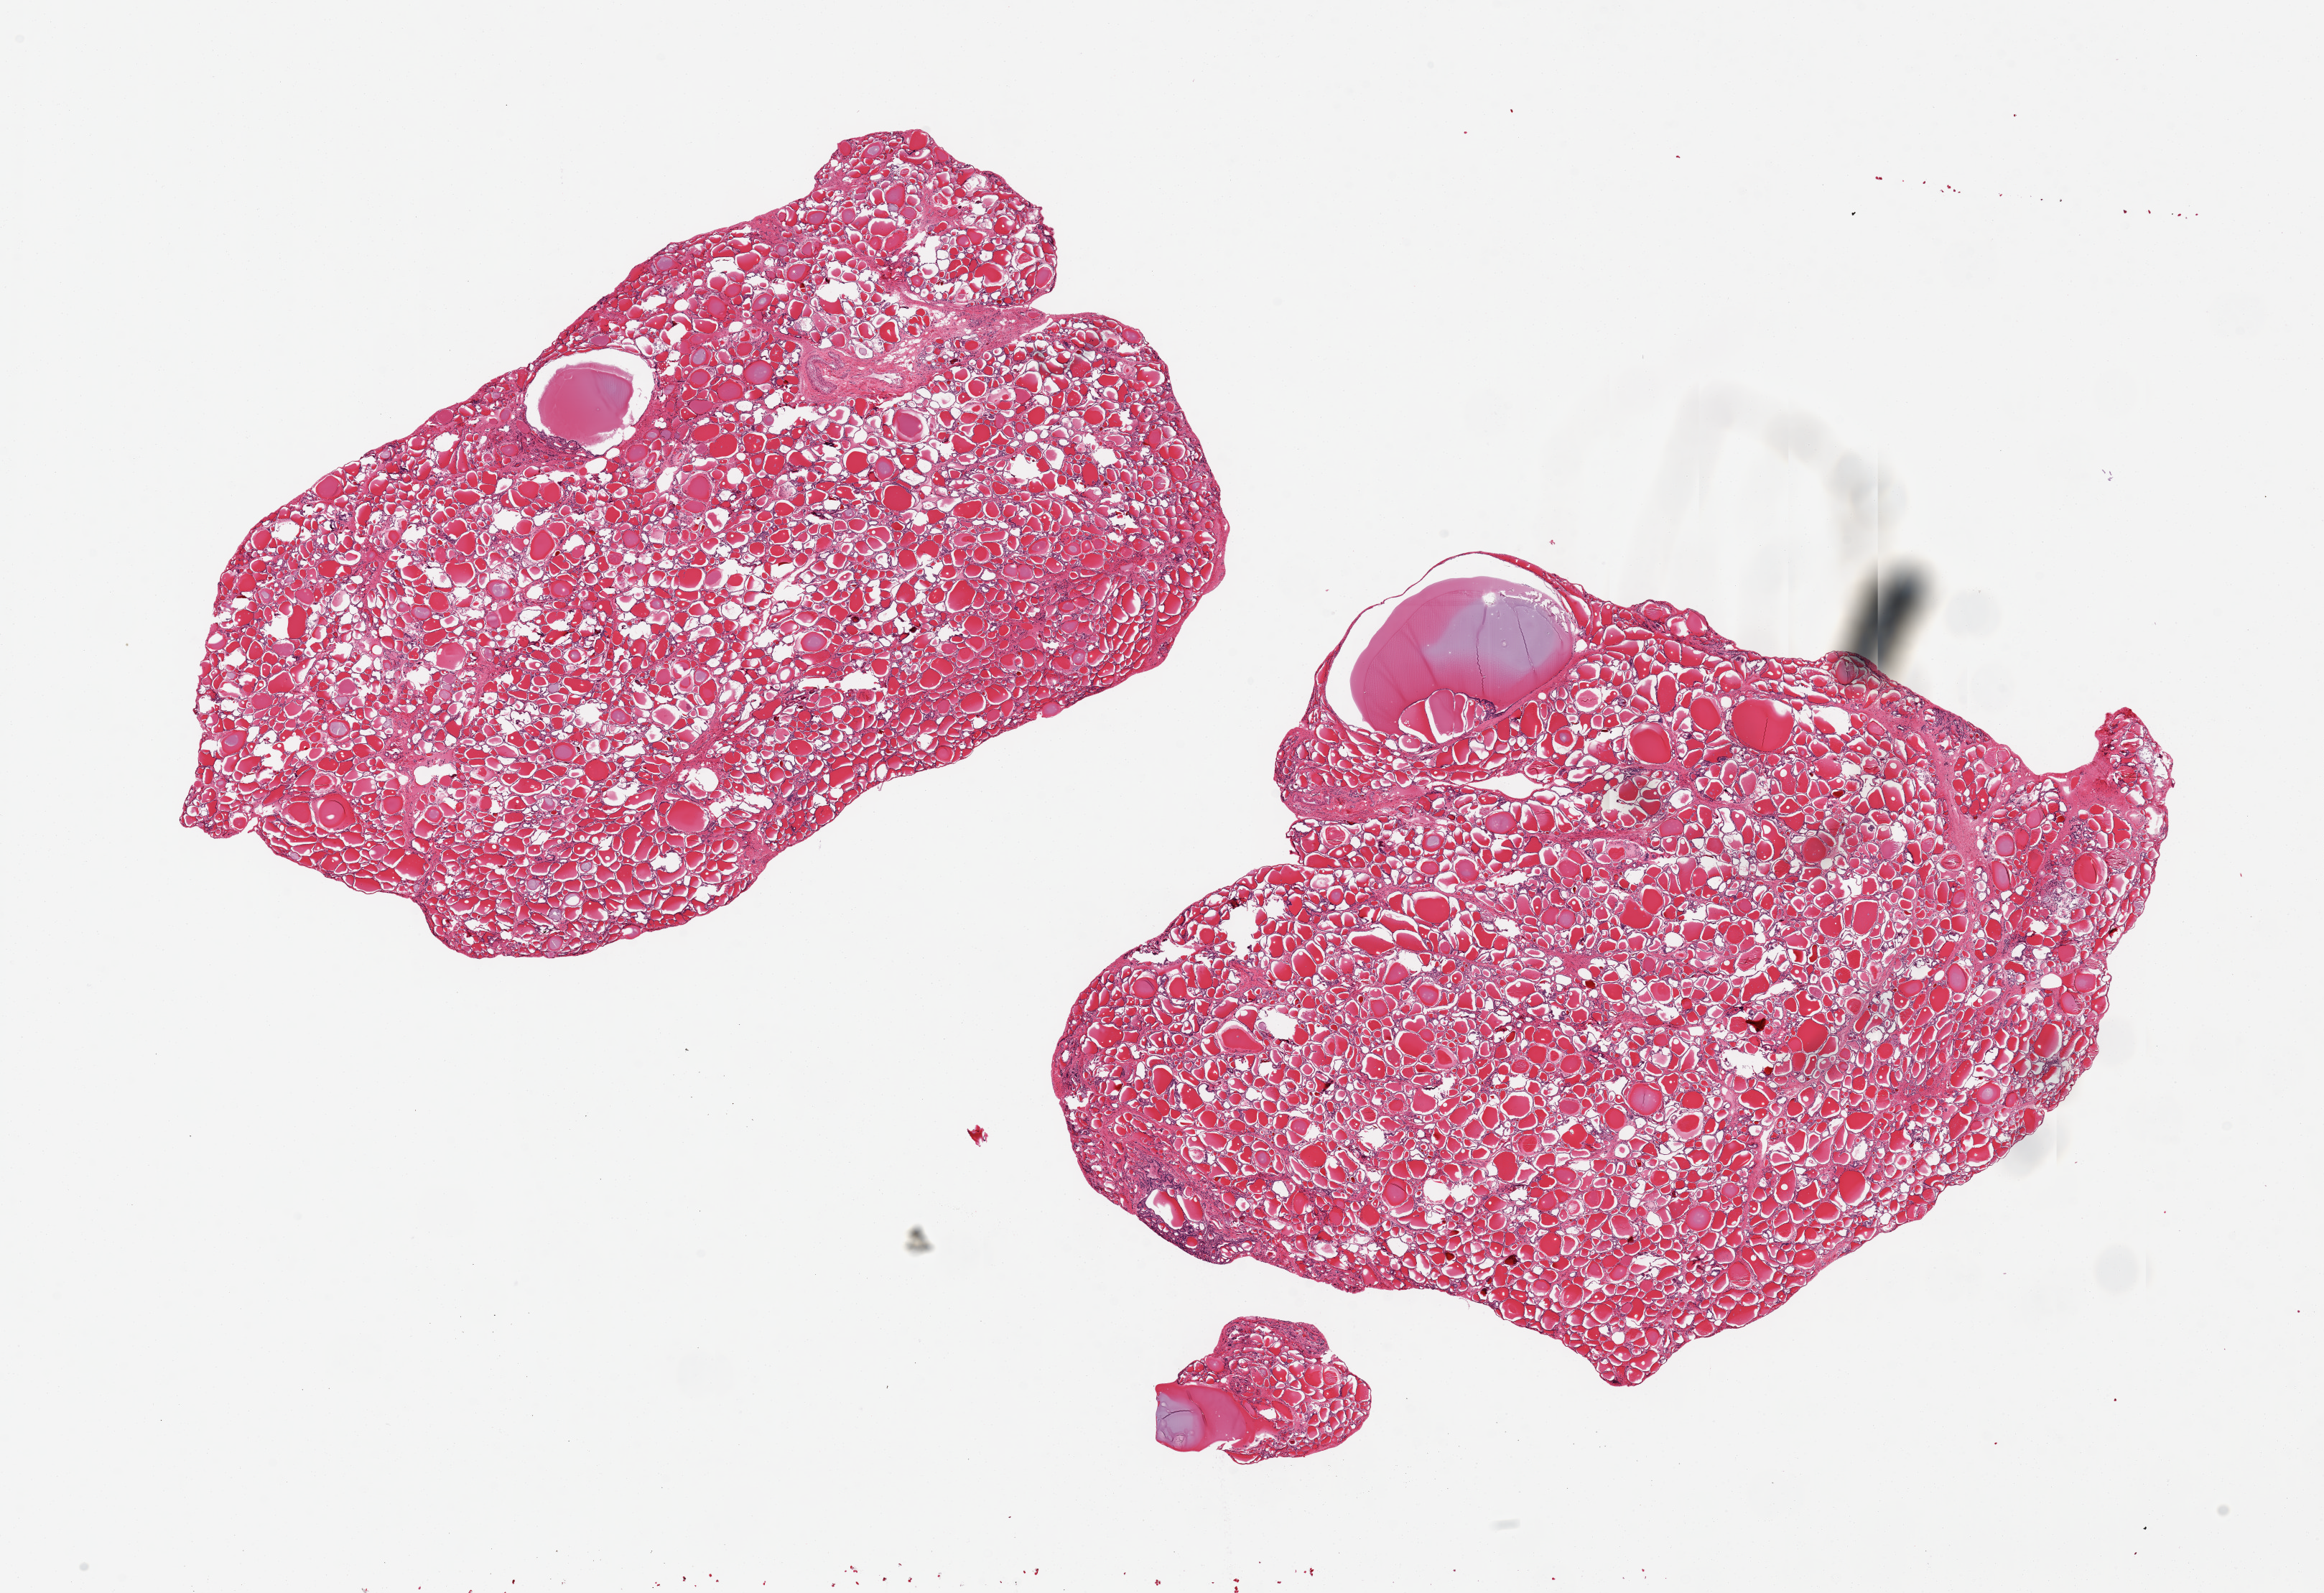
H&E whole-slide image, brightfield, a low-resolution overview of the entire scanned area, about 25.6 x 17.5 mm; PAXgene-fixed, paraffin-embedded tissue; target tissue: thyroid; tissue donor sample. Female donor.
Review note (as recorded): 2 ~9x7mm aliquots. Scattered colloid cysts, up to 3mm in dimensions.